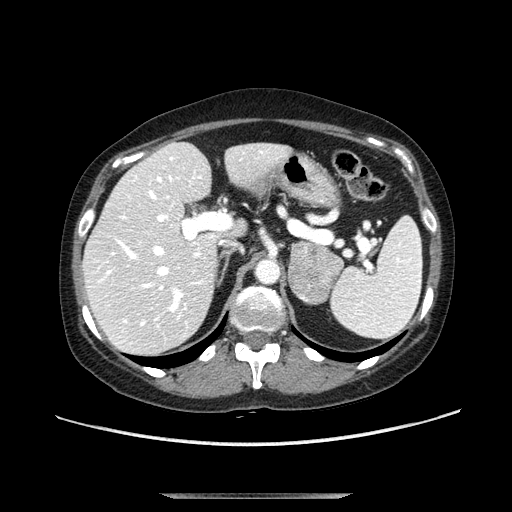
Contrast-enhanced abdominal CT, one axial slice. Position 70 of 107 along the scan axis. Soft-tissue window (W 400 / L 40 HU). 2.5 mm slice thickness. 512 × 512 image matrix, field of view 380 × 380 mm. Female patient. From the clinical record (not read from this slice): diagnosis: adrenocortical carcinoma; tumour side: left adrenal; tumour size at pathology: 7.5 cm; Ki-67 index: 9 %; stage (as recorded): 3.
Annotated regions visible in this slice (semi-automatically segmented with operator editing):
- mass: bounding box [x1, y1, x2, y2] px = [288, 243, 344, 303]